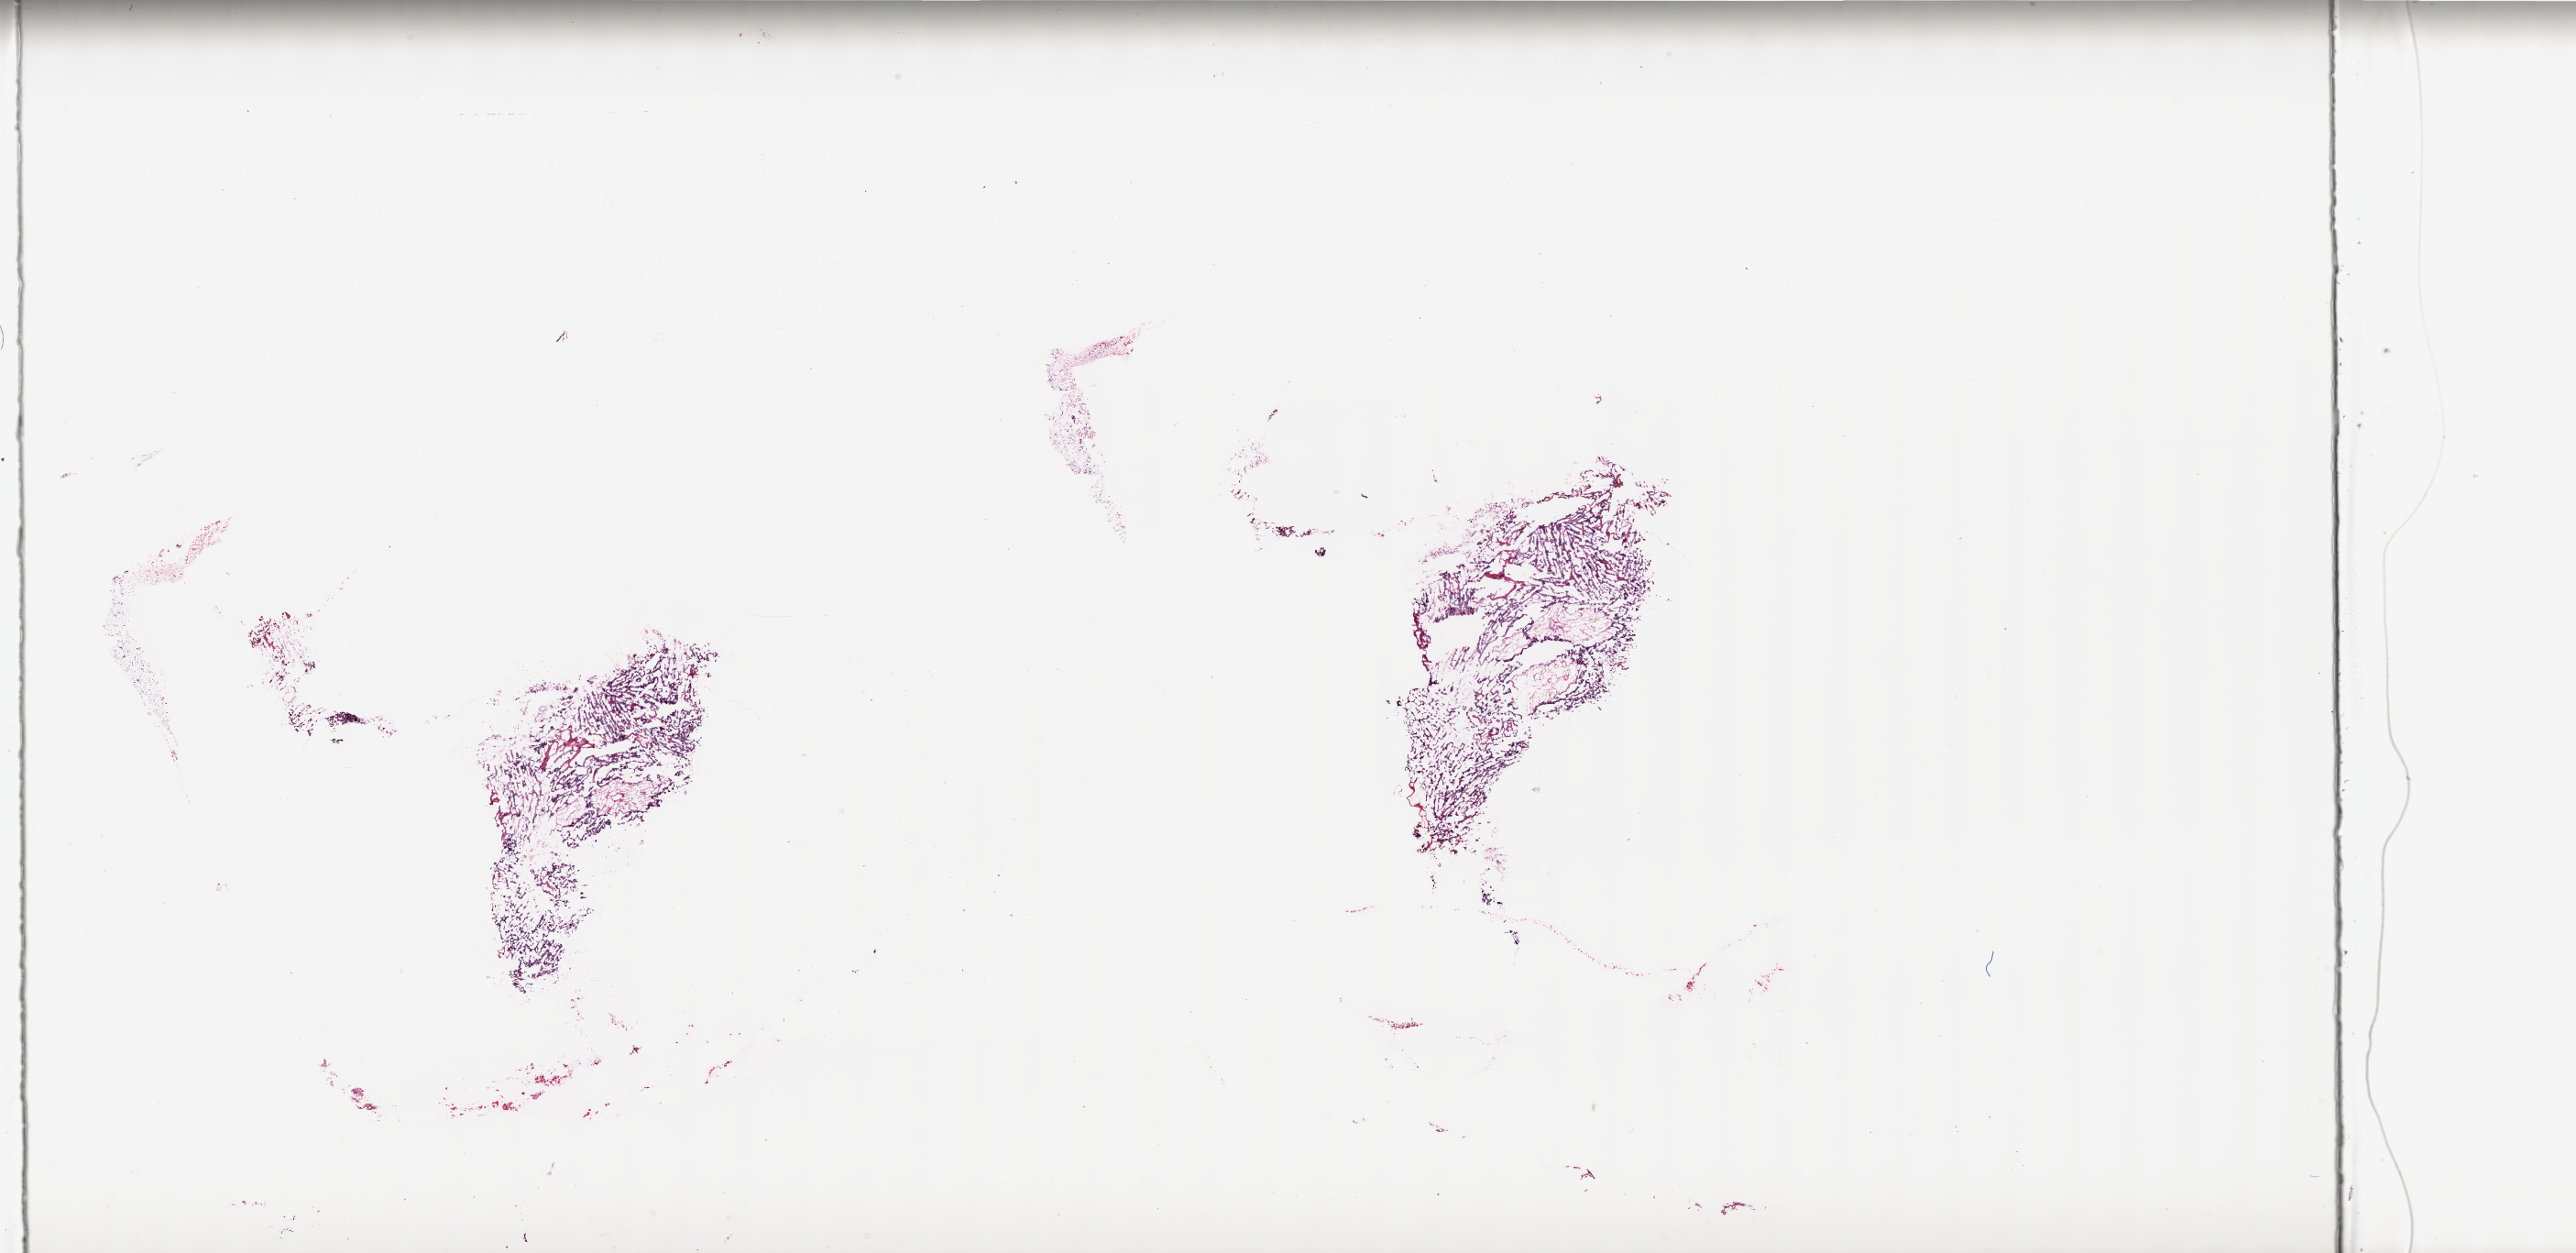
H&E whole-slide image — shown as a low-resolution overview of the whole scanned area (about 44.9 x 21.8 mm, slide scanned at 20x); frozen section from the top of the tissue portion; sample: primary tumour, ovary. Female patient; age at initial diagnosis 61 years. Composition of this section per pathologist review: tumour cells 93%, tumour nuclei 99%.
Diagnosis: Serous cystadenocarcinoma, NOS.